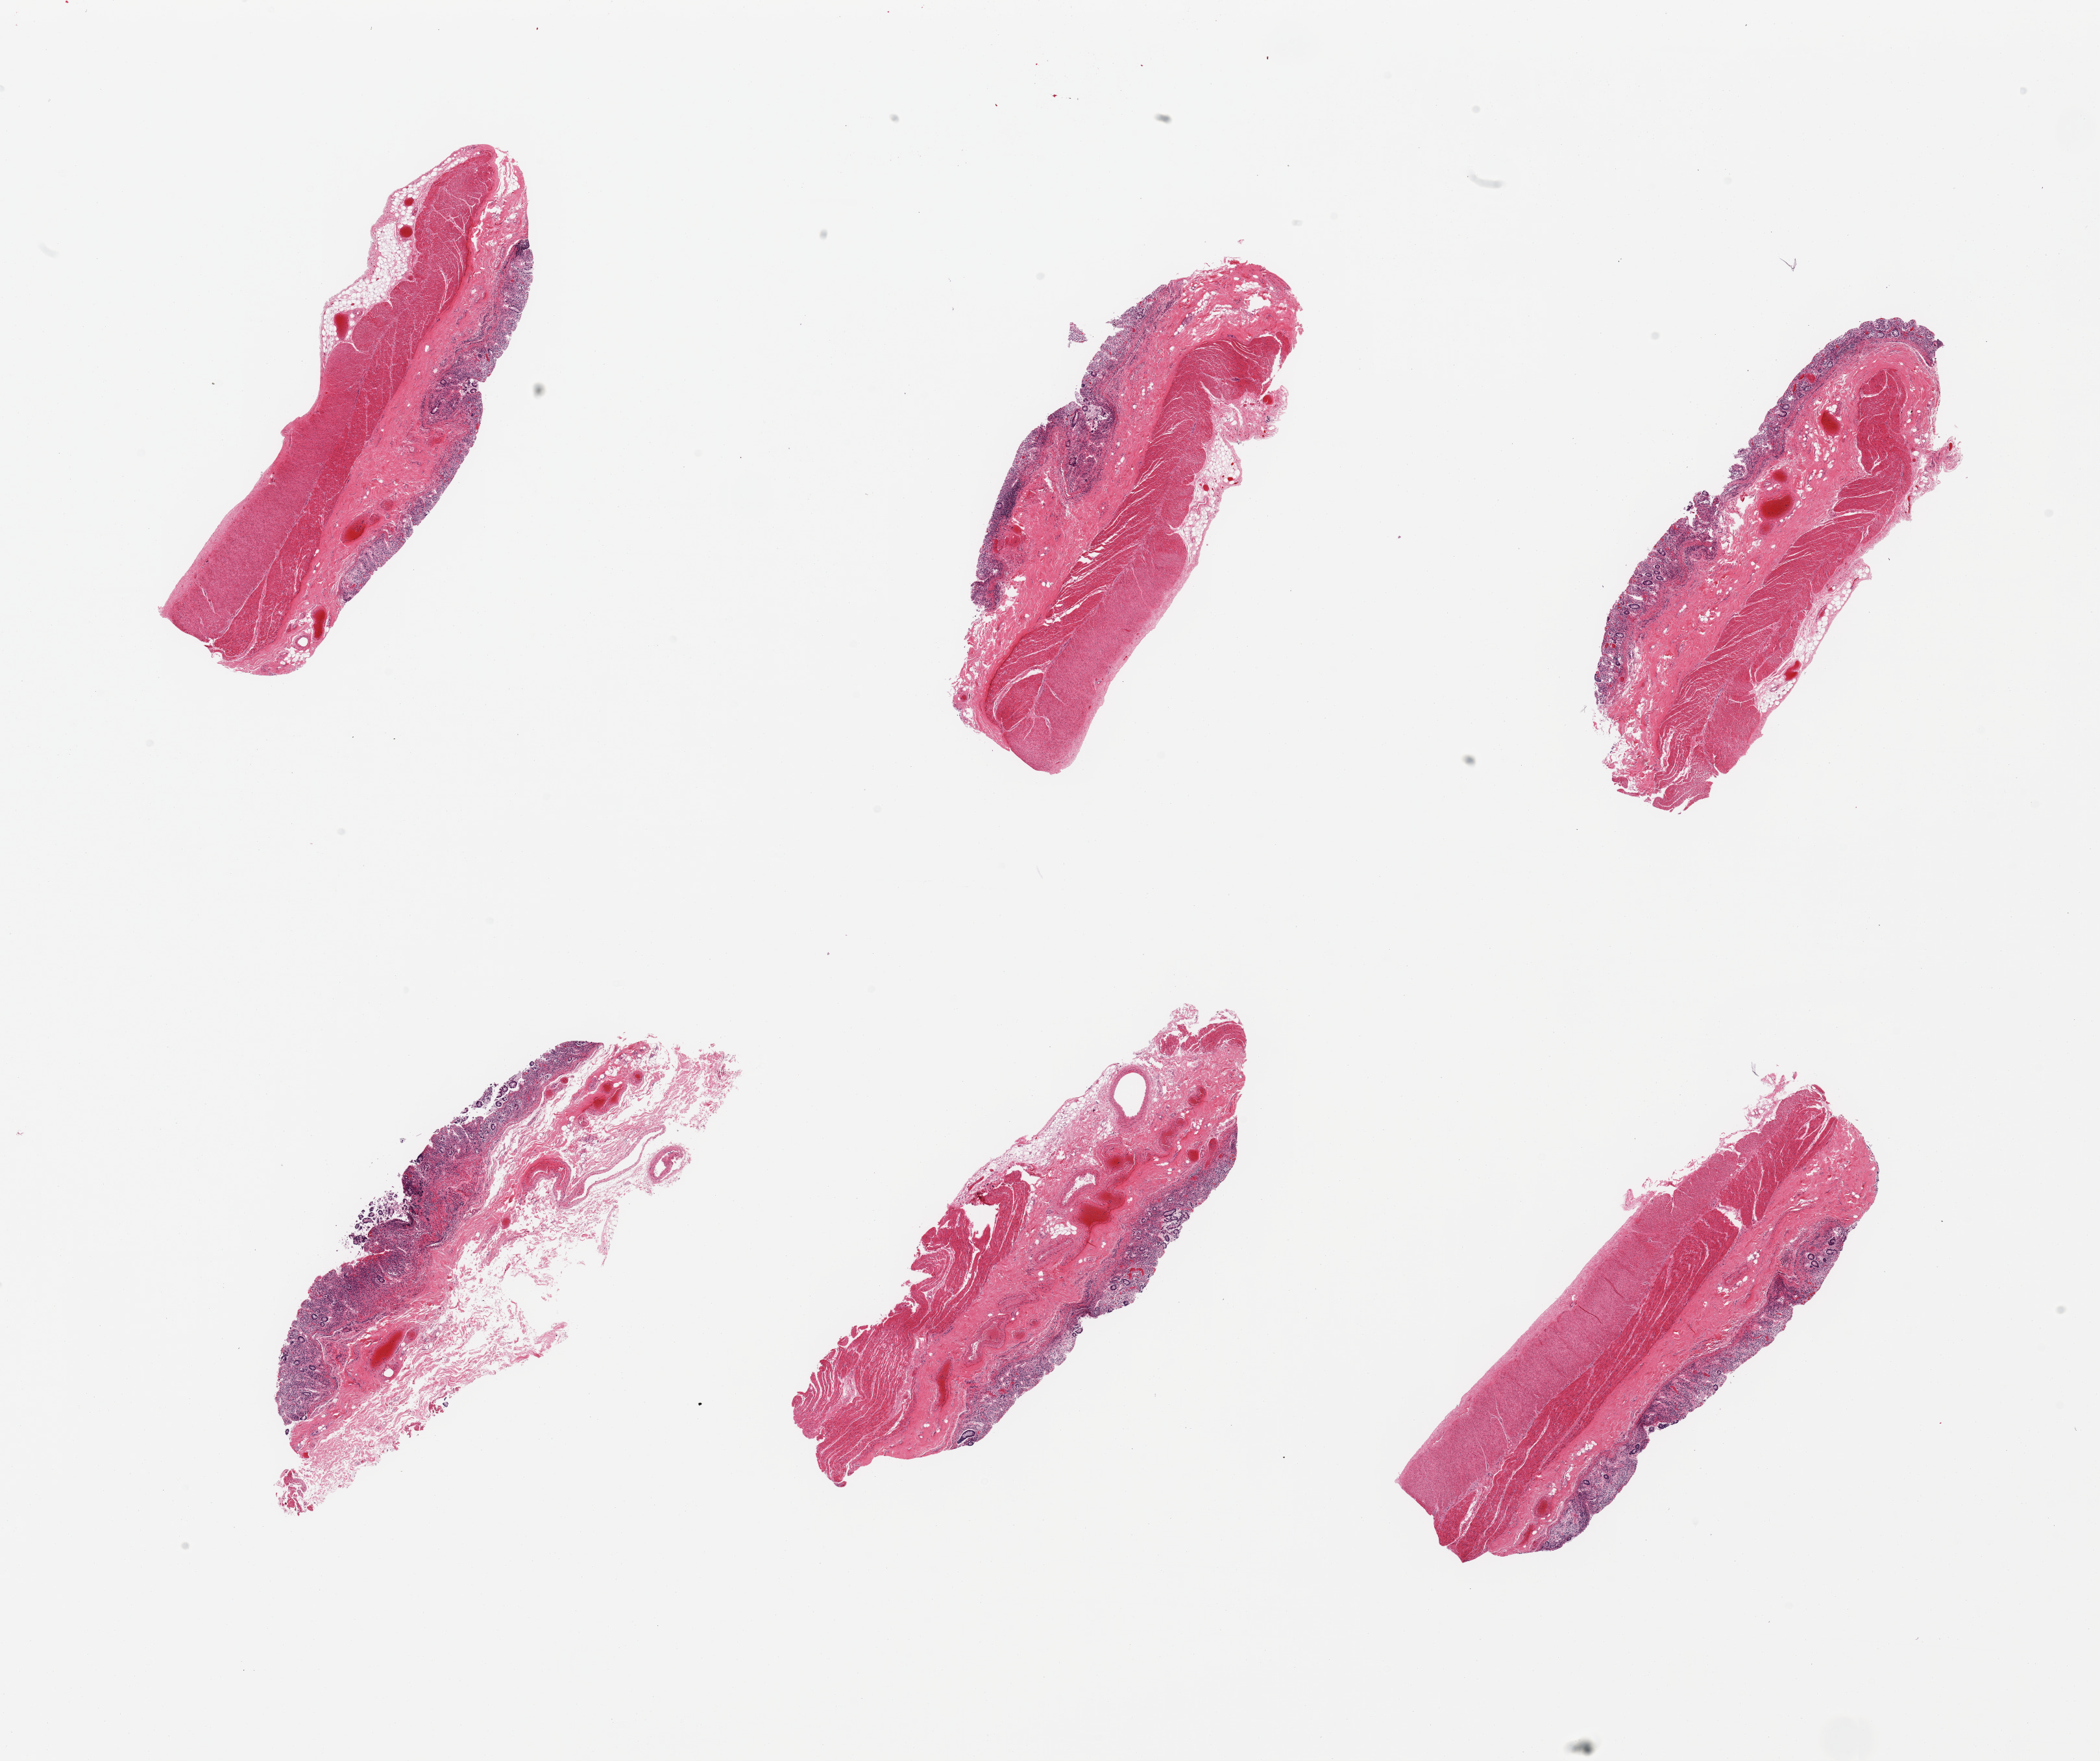
Whole-slide image, hematoxylin and eosin (H&E) stain — a low-resolution overview of the entire scanned area, about 25.6 x 21.5 mm, PAXgene-fixed paraffin-embedded (PFPE) section, target tissue: transverse colon, donor tissue sample. Donor: female.
• review note (as recorded): 6 pieces, target mucosa up to ~0.4mm, advanced autolysis